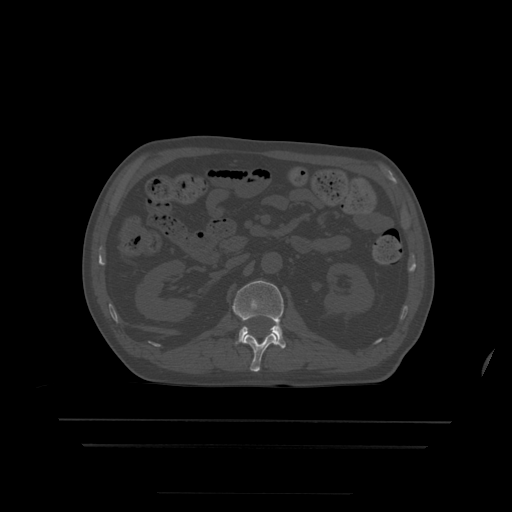
CT including the spine, one axial slice. Slice 156 of 522 in the series (ordered by position). Bone window (W 1800 / L 400 HU). 1.25 mm slice thickness. 512 × 512 image matrix, field of view 436 × 436 mm. Patient age 68 years. Case-level facts recorded for this patient, not image findings: primary cancer: urothelial.
Outlined on this slice (semi-automatic segmentation, software-assisted and operator-edited):
- L1 vertebra: bounding box <244,333,277,372> (left, top, right, bottom; pixels)
- L2 vertebra: <233,281,286,349>